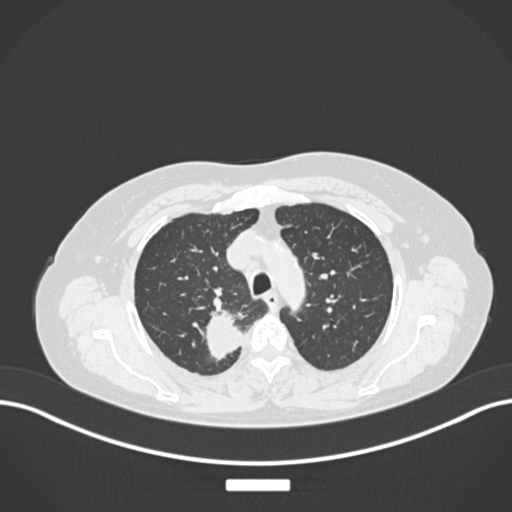
Chest CT, one axial slice; position 196 of 237 along the scan axis; 120 kVp; lung window (W 1500 / L -600 HU); 1 mm slice thickness; 512 × 512 image matrix, field of view 400 × 400 mm. Patient: female, 62 years. Case-level facts recorded for this patient, not image findings: clinical TNM (as recorded): T1c N1 M0.
Outlined on this slice (rectangle marked by the reading radiologist):
- lung tumour (recorded histology: squamous cell carcinoma): bounding box (x1, y1, x2, y2) in pixels: (202, 311, 244, 368)